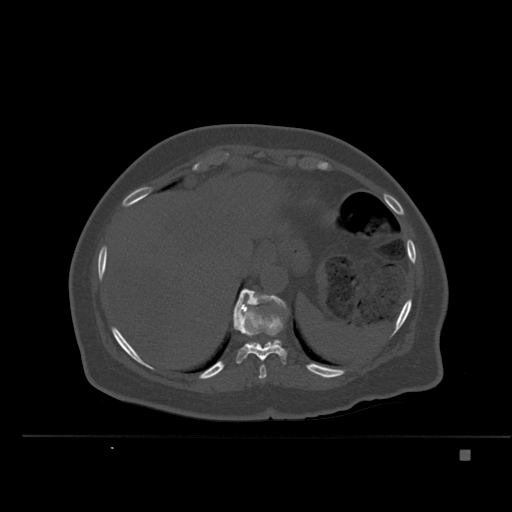
CT including the spine, one axial slice. Position 282 of 477 along the scan axis. Bone window (W 1800 / L 400 HU). 512 × 512 image matrix, field of view 422 × 422 mm. Patient: female, 74 years. From the clinical record (not read from this slice): primary cancer: colon.
Structures marked on this image (semi-automatically segmented with operator editing):
- T10 vertebra: bounding box (x1, y1, x2, y2) in pixels: (233, 300, 287, 365)
- T11 vertebra: (234, 288, 287, 346)
- T9 vertebra: (259, 365, 267, 379)